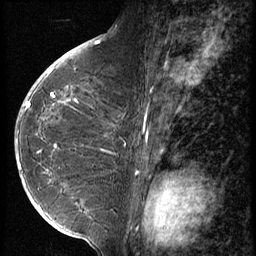
Breast MRI (dynamic contrast-enhanced), one sagittal slice; position 34 of 56 along the scan axis; 3 images stored at this slice position (order not interpretable as contrast timing); 1.5 T; TE 4.2 ms, TR 9 ms; 2.5 mm slice thickness; 256 × 256 image matrix, field of view 180 × 180 mm. Patient: female, 49 years. From the clinical record (not read from this slice): setting: breast cancer imaged before/during neoadjuvant chemotherapy; receptor status: HER2-positive.
Outlined on this slice (semi-automatically segmented with operator editing):
- analysis volume of interest (the breast-tissue region the enhancement analysis was run in; not a lesion): bounding box [x1, y1, x2, y2] px = [15, 116, 19, 166]
- tumour enhancement mask (voxels above the 140 % enhancement threshold inside the analysis volume of interest): [17, 157, 19, 160]